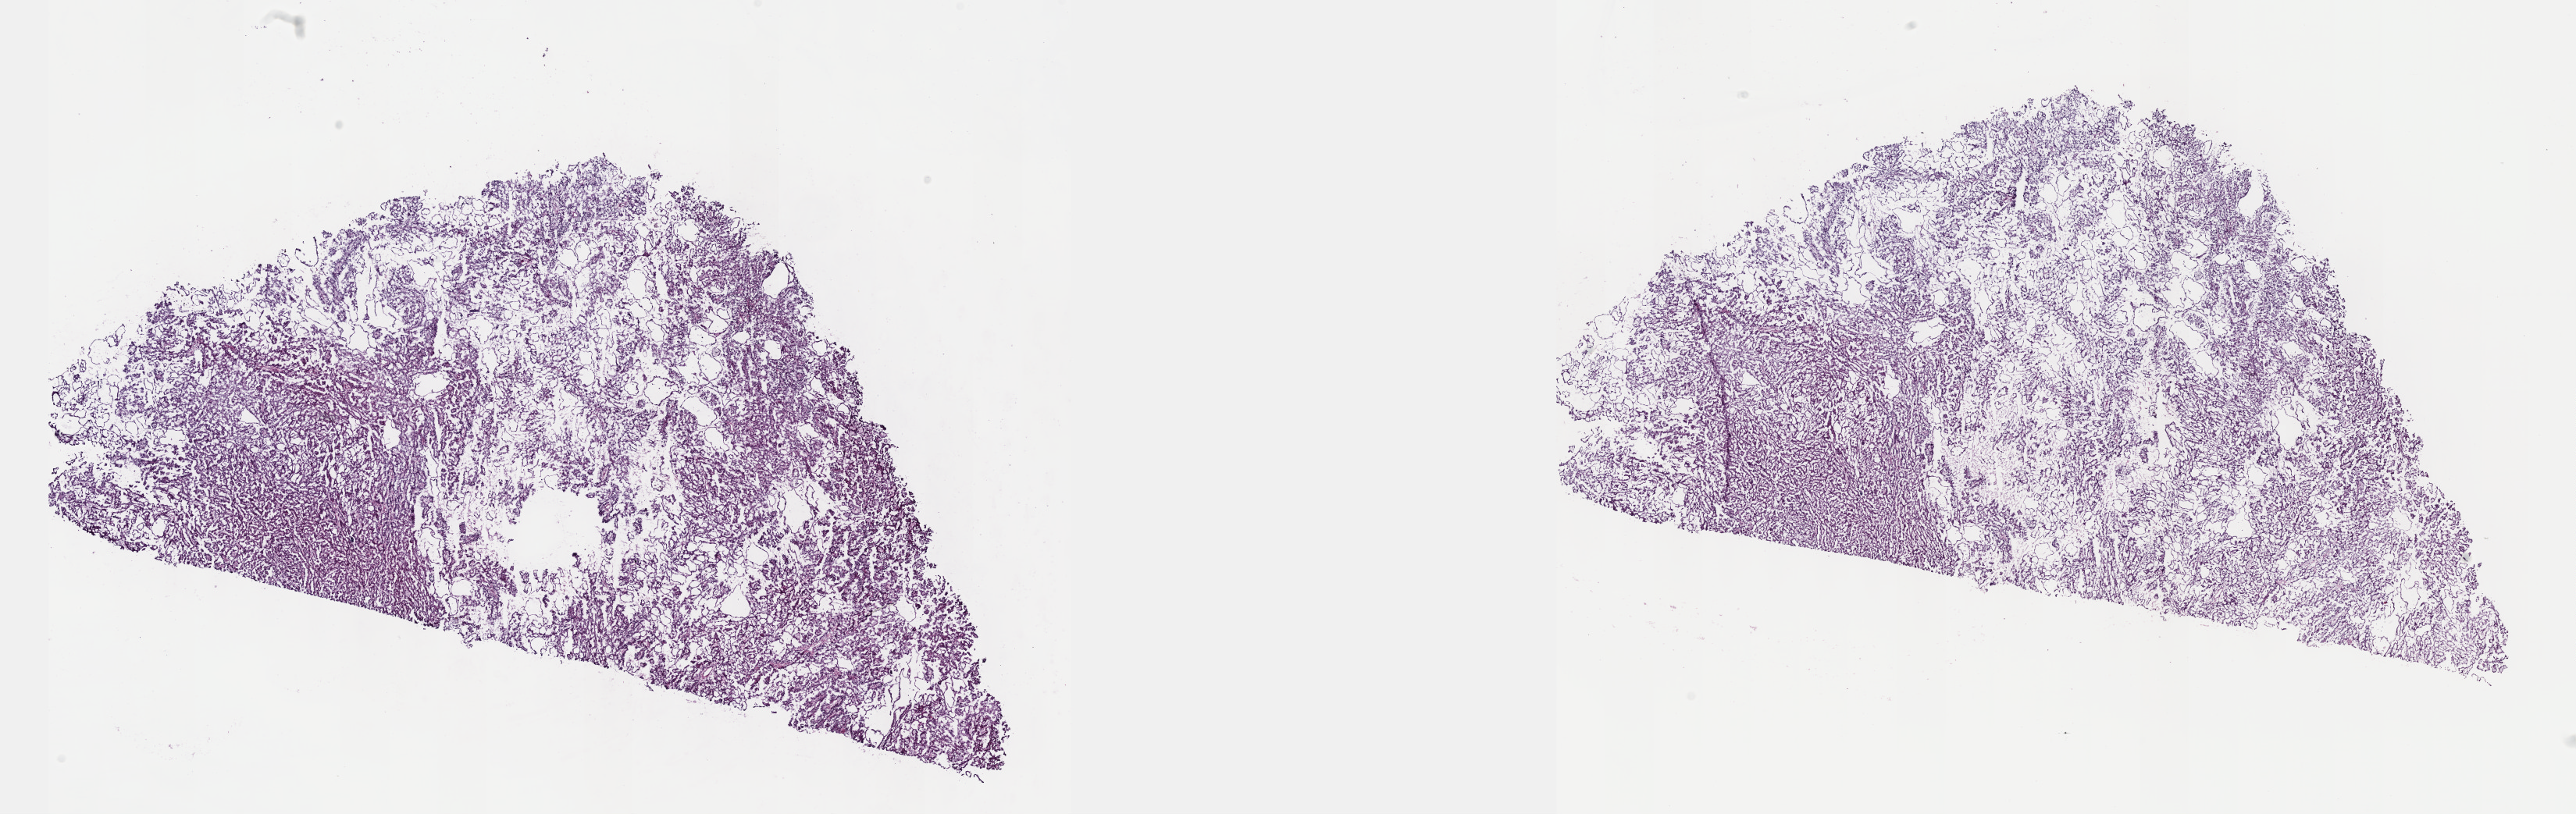
Digitized H&E-stained tissue section (whole slide), whole scanned area (about 26.7 x 8.4 mm, slide scanned at 40x) shown as a low-resolution overview. Frozen section. Kidney, primary tumour sample. Male, age 60 years at initial diagnosis. Slide review estimates, as recorded: tumour cells 100%, tumour nuclei 75%, normal cells 0%, stromal cells 0%, necrosis 0%. Infiltration values recorded for this section: lymphocyte infiltration 1%, monocyte infiltration 3%, neutrophil infiltration 0%.
• laterality: right
• pathologic diagnosis: Papillary adenocarcinoma, NOS
• AJCC pathologic stage: I (6th edition)